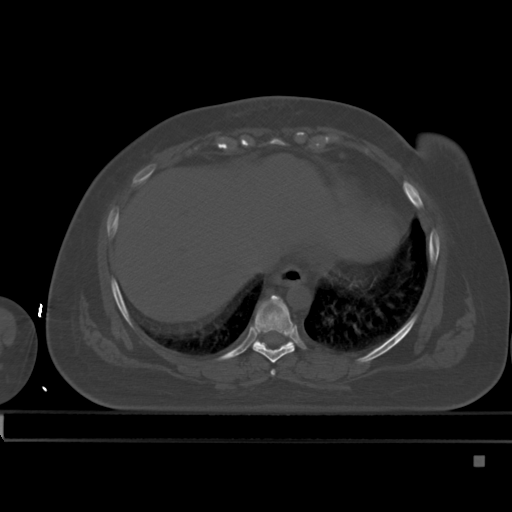
CT including the spine, one axial slice. Slice 273 of 495 in the series (ordered by position). Bone window (W 1800 / L 400 HU). 1.5 mm slice thickness. 512 × 512 image matrix, field of view 404 × 404 mm. Female patient, age 33 years. Case-level facts recorded for this patient, not image findings: primary cancer: breast; vertebrae with lytic lesions (as recorded): T1.
Outlined on this slice (semi-automatically segmented with operator editing):
- T7 vertebra: bounding box <270,370,276,376> (left, top, right, bottom; pixels)
- T8 vertebra: <253,295,295,363>
- T9 vertebra: <253,336,293,347>